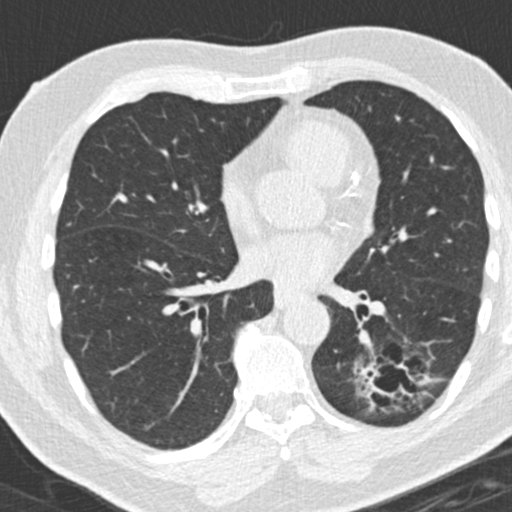
Axial slice from a low-dose chest CT screening exam. Third screening round (two years after baseline). Lung window (W 1500 / L -600 HU). 2 mm slice thickness. Slice 90 of 180 in the series. 512 × 512 image matrix. Male, age 66 years at enrolment. Former smoker at enrolment.
Expert-annotated lung lesion, bounding box (x1, y1, x2, y2) in pixels: (356, 348, 426, 427). The exam's reader record, not a measurement of the box and not confirmed to be the same lesion: non-calcified nodule or mass ≥4 mm, left lower lobe, 31 × 24 mm, spiculated (stellate) margins, pre-existing on the prior screen: yes; interval growth: yes. Lung cancer was diagnosed 56 days after this screen: adenocarcinoma, NOS, left lower lobe, poorly differentiated (G3), stage IB (AJCC 6th edition), 38 mm at pathology.